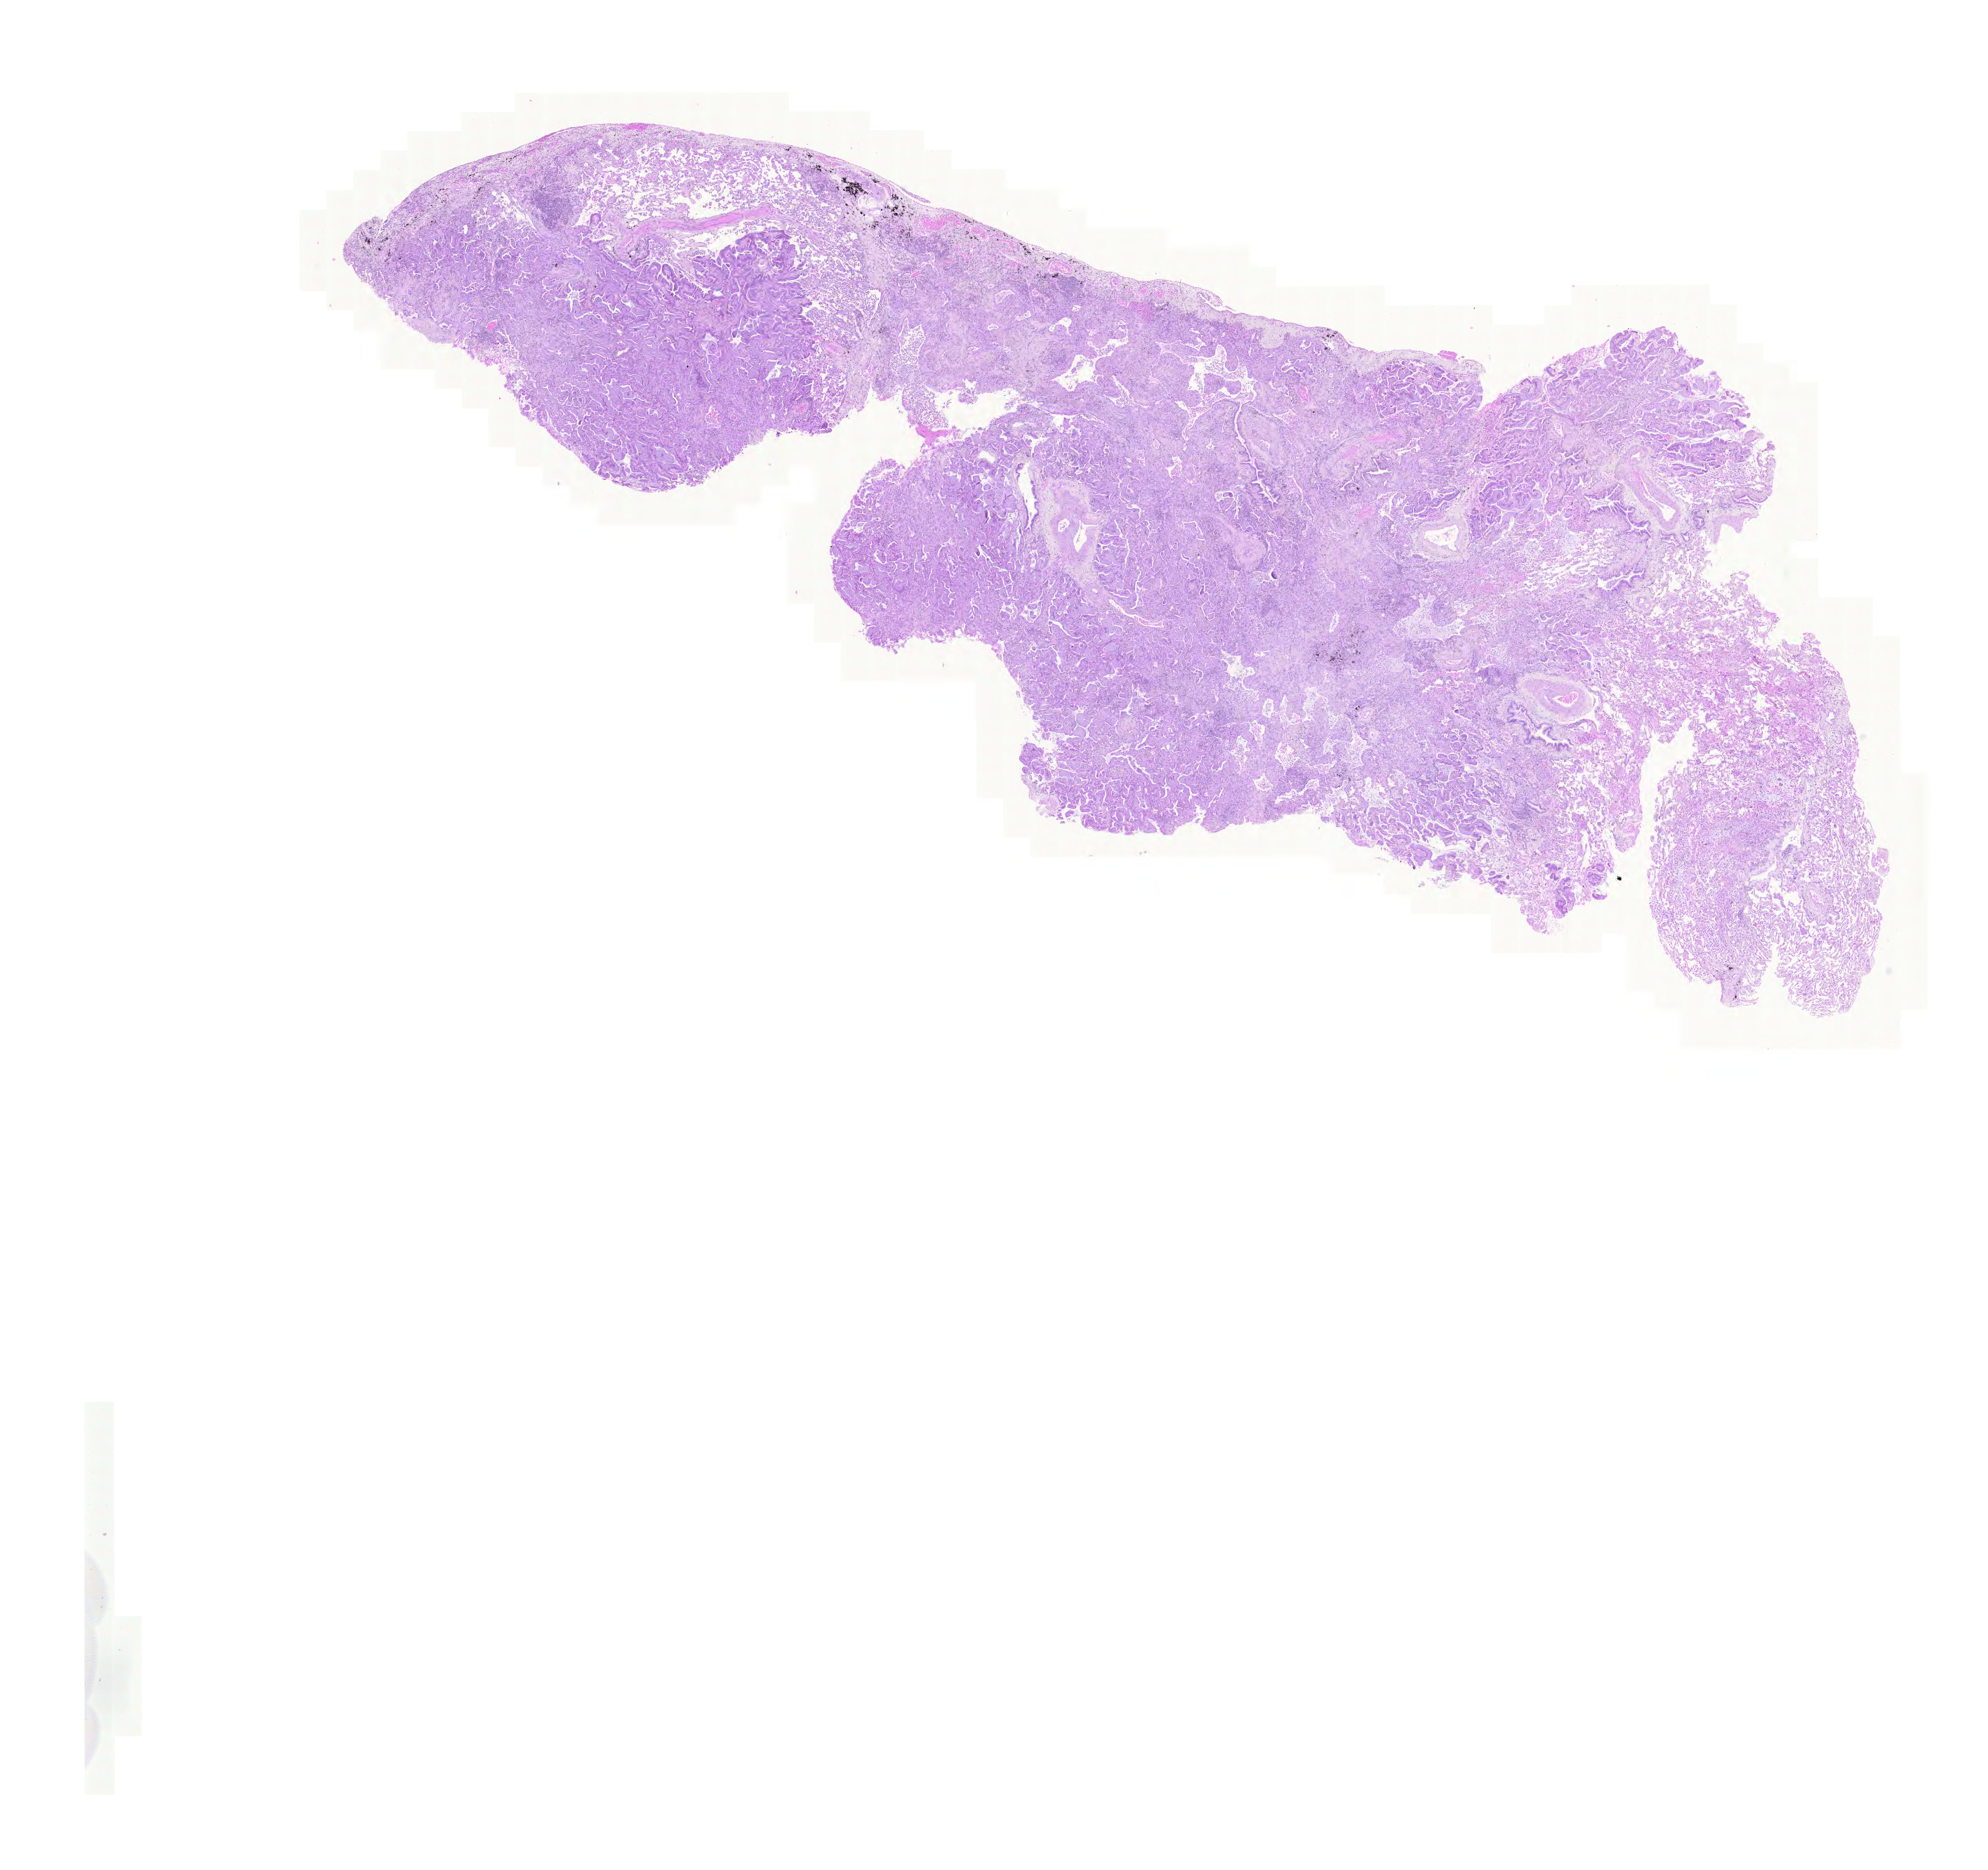
H&E-stained whole-slide image, shown as a low-resolution overview of the whole scanned area (about 21.1 x 19.8 mm, slide scanned at 20x), formalin-fixed paraffin-embedded (FFPE) diagnostic section, primary tumour sample from the lung. Male patient; age at initial diagnosis 76 years.
AJCC pathologic stage: IB. Laterality: right. Diagnosis: Adenocarcinoma with mixed subtypes (upper lobe, lung).